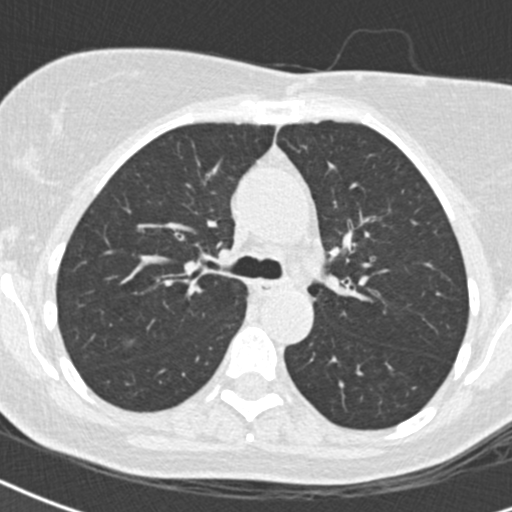
Low-dose screening chest CT, axial slice; first (baseline) screen; lung window (W 1500 / L -600 HU); 2 mm slice thickness; 120 kVp; slice 61 of 184 in the series. Female participant, aged 57 years at enrolment. Current smoker at enrolment.
Expert-annotated lung lesion, bounding box (x1, y1, x2, y2) in pixels: (111, 332, 142, 361). The exam's reader record, not a measurement of the box and not confirmed to be the same lesion: non-calcified nodule or mass ≥4 mm, left upper lobe, 10 × 9 mm, spiculated (stellate) margins, soft tissue attenuation. Note: the box lies in the patient's right hemithorax on this image, whereas the reader's record names the left lung; they may be different findings. Official screen result: positive, change unspecified: nodule(s) >= 4 mm or enlarging nodule(s), mass(es), or other non-specific abnormalities suspicious for lung cancer. Later outcome: lung cancer diagnosed 153 days after this screen — non-small cell carcinoma, right upper lobe, stage IA (AJCC 6th edition), 13 mm at pathology.